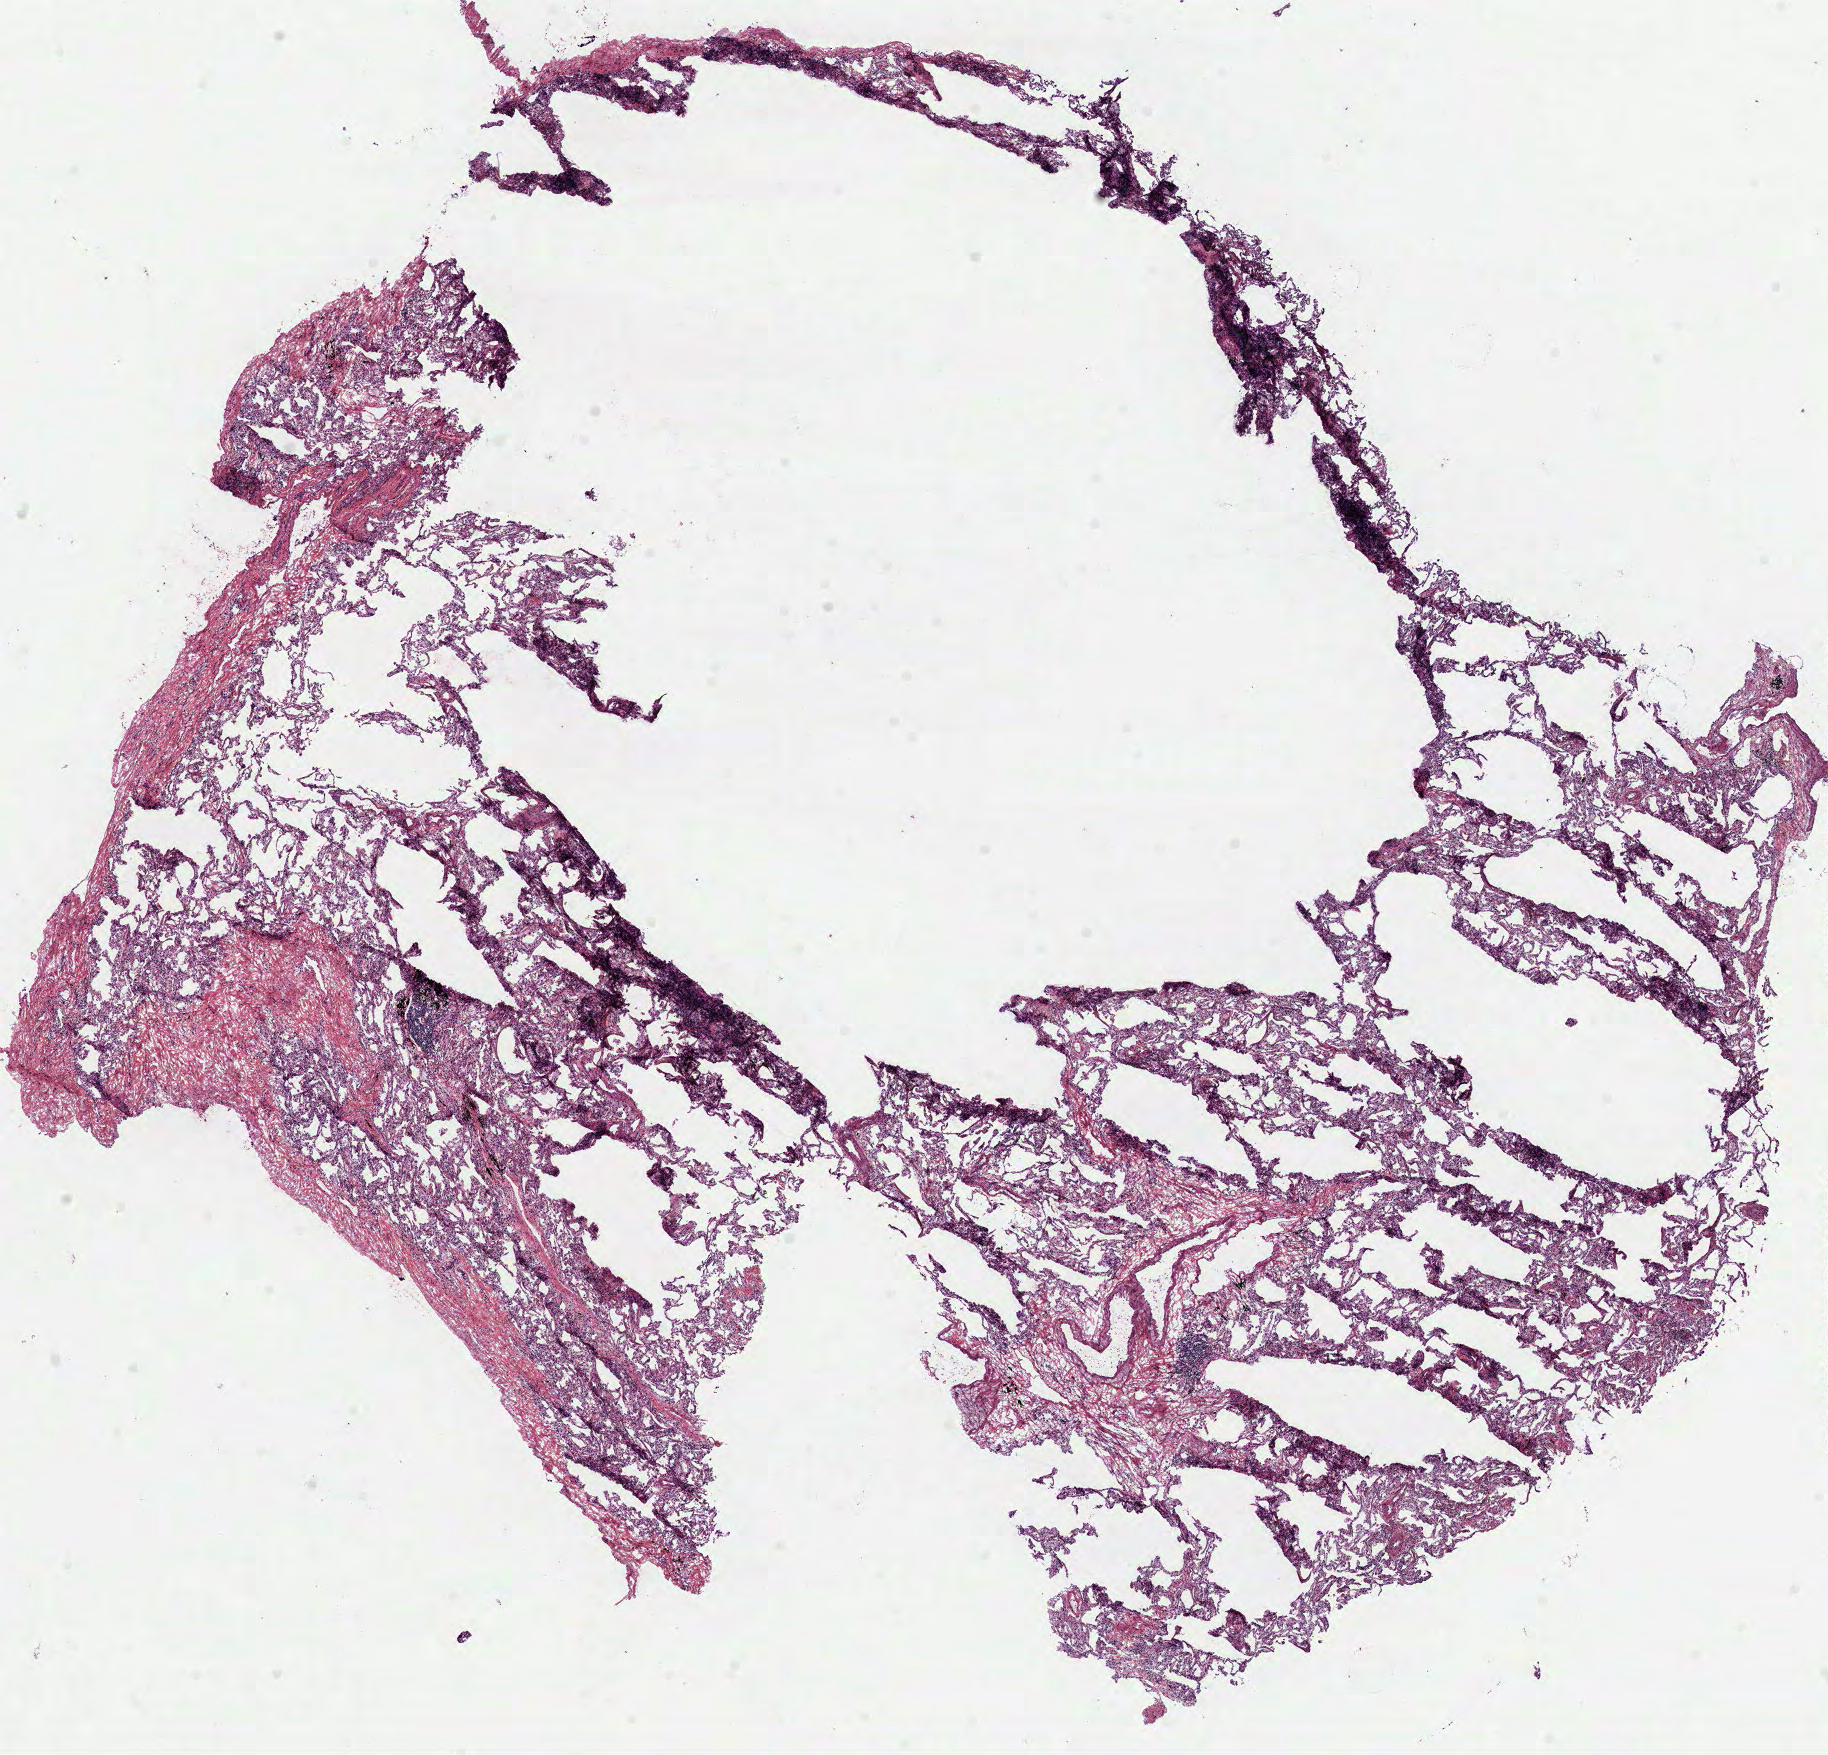
Whole-slide histology image, H&E, low-resolution overview of the scanned area, about 14.7 x 14.2 mm (acquisition: 40x scan); frozen section; lung, solid tissue normal (non-tumour tissue) sample. Female, age 75 years at initial diagnosis.
• this section: solid tissue normal (non-tumour) sample from the same patient
• patient diagnosis: Adenocarcinoma, NOS (upper lobe, lung)